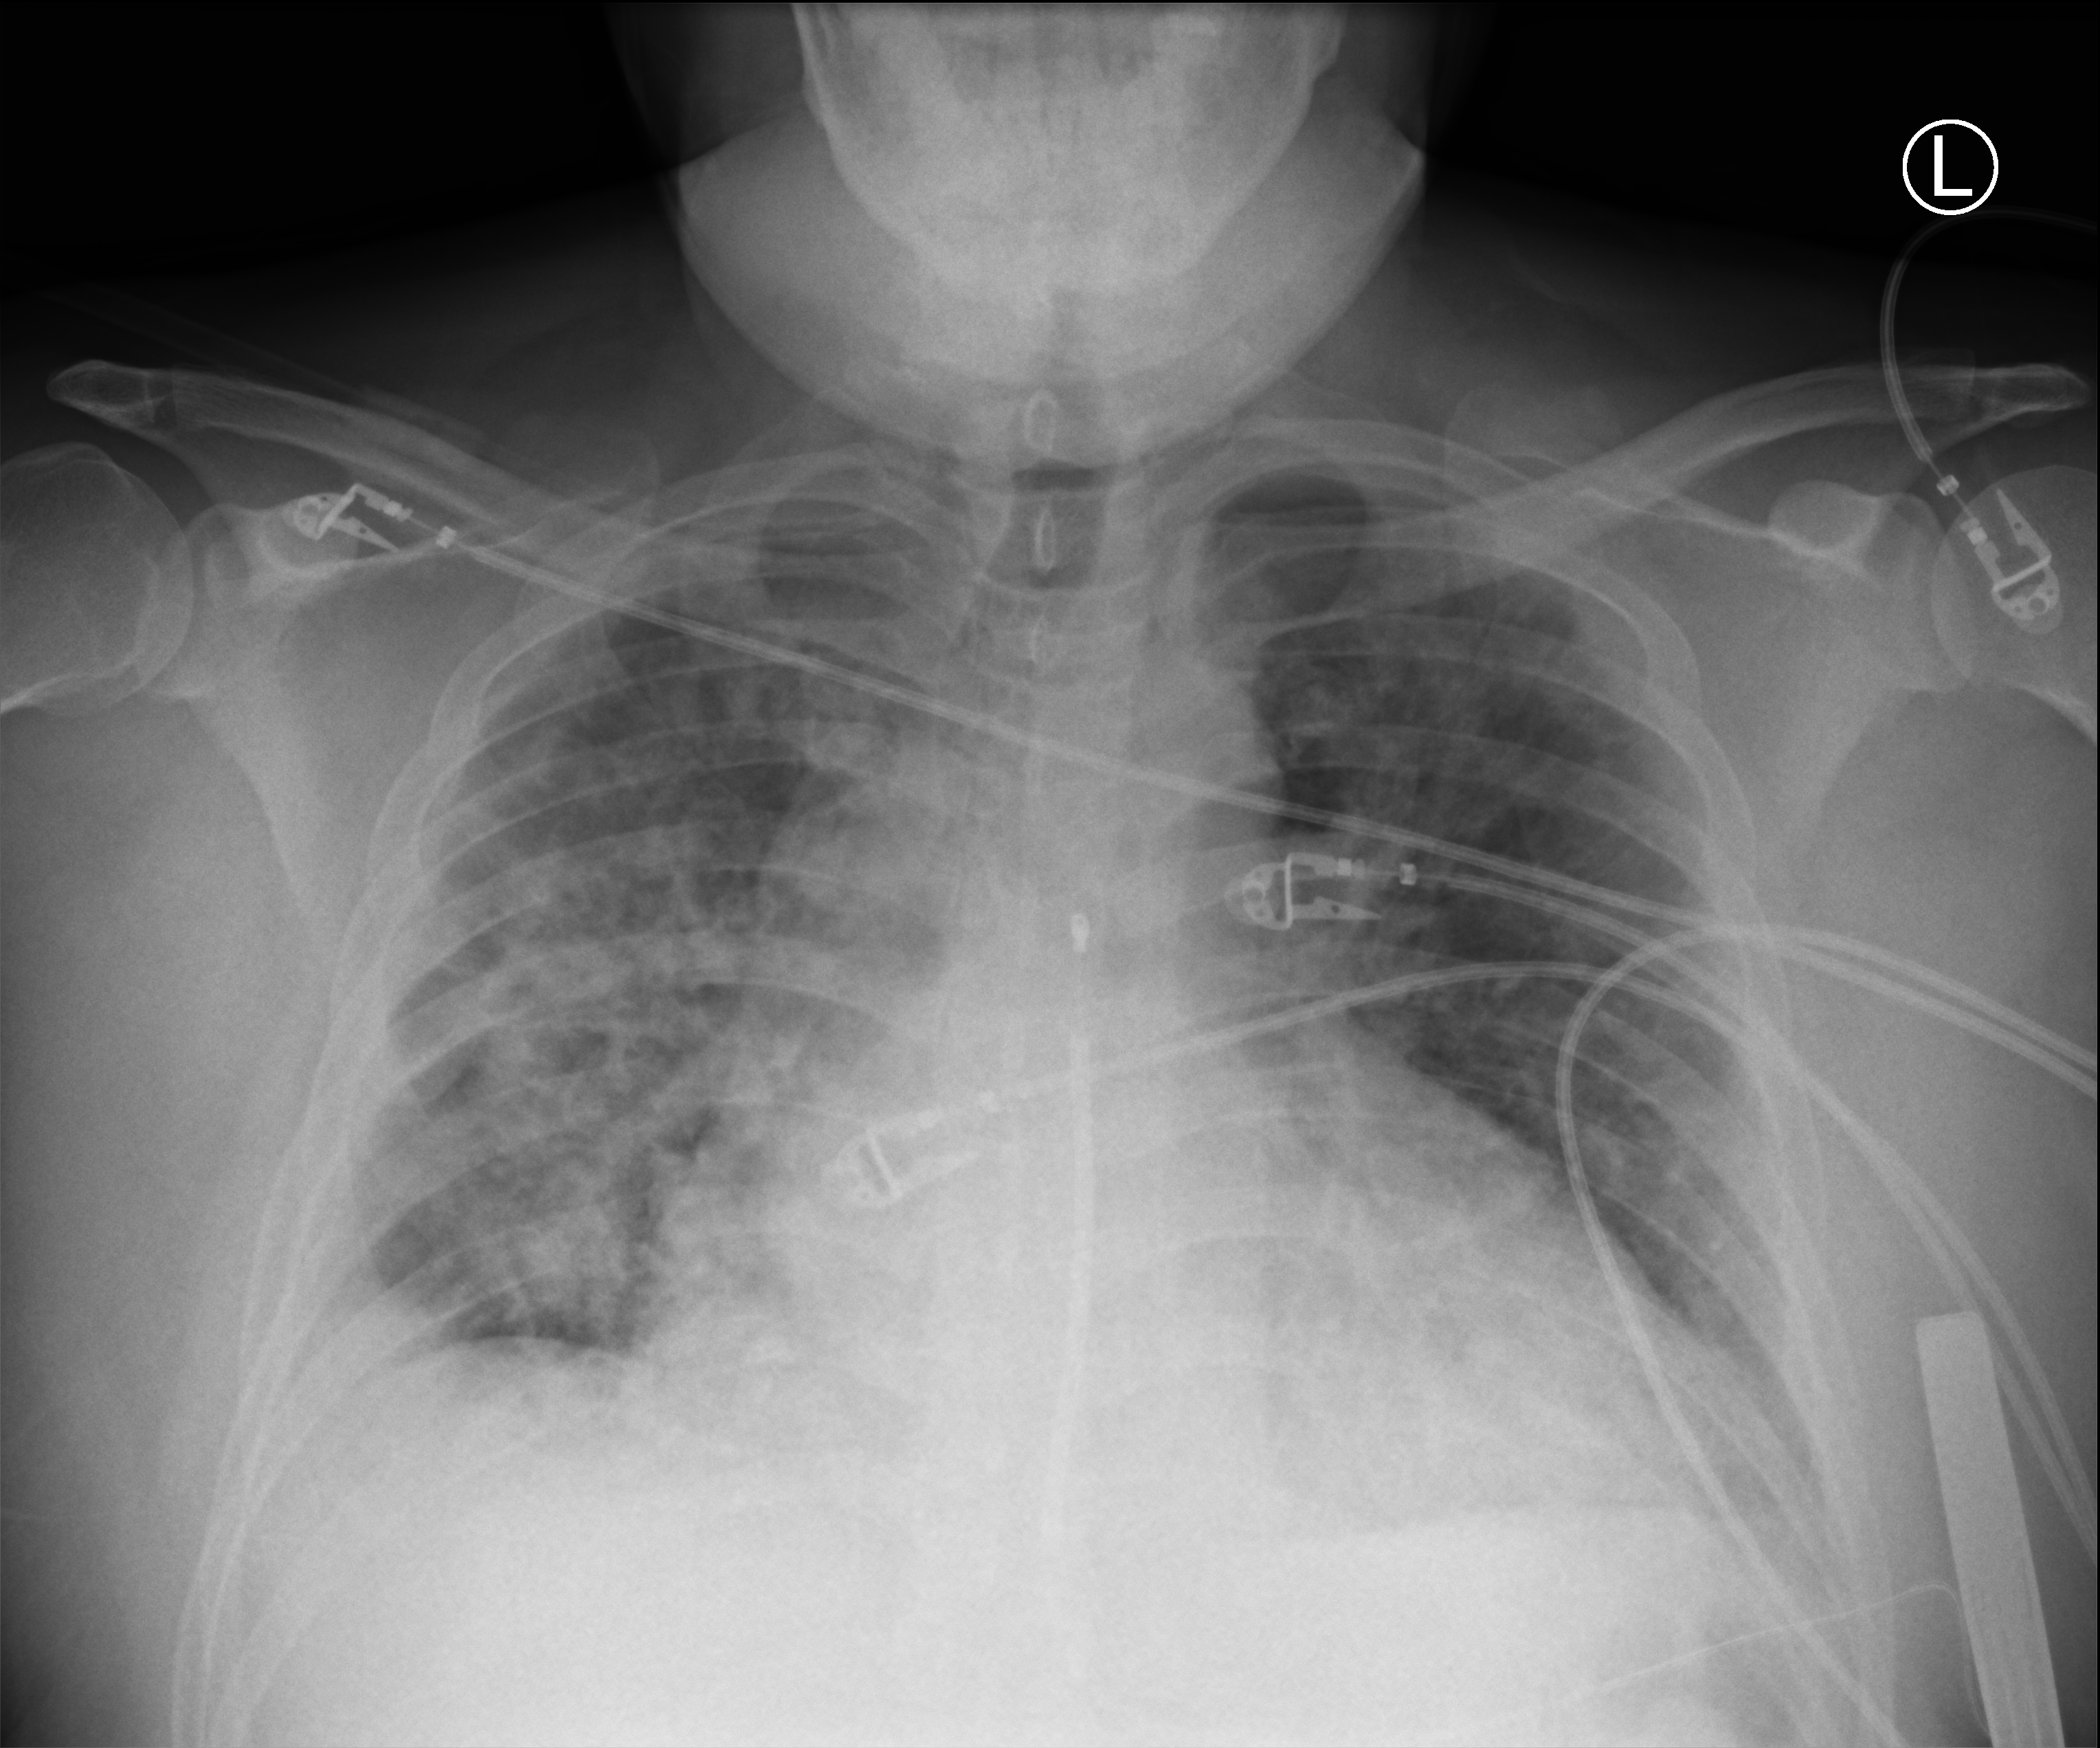
Portable chest radiograph; anteroposterior (AP) projection. Male patient hospitalised with COVID-19, age 18–59 years.
Admission-level facts for this patient (not findings on this image; timing relative to this image not recorded):
- admitted to intensive care during this hospital stay: no
- mechanically ventilated during this hospital stay: no
- length of hospital stay: 19 days